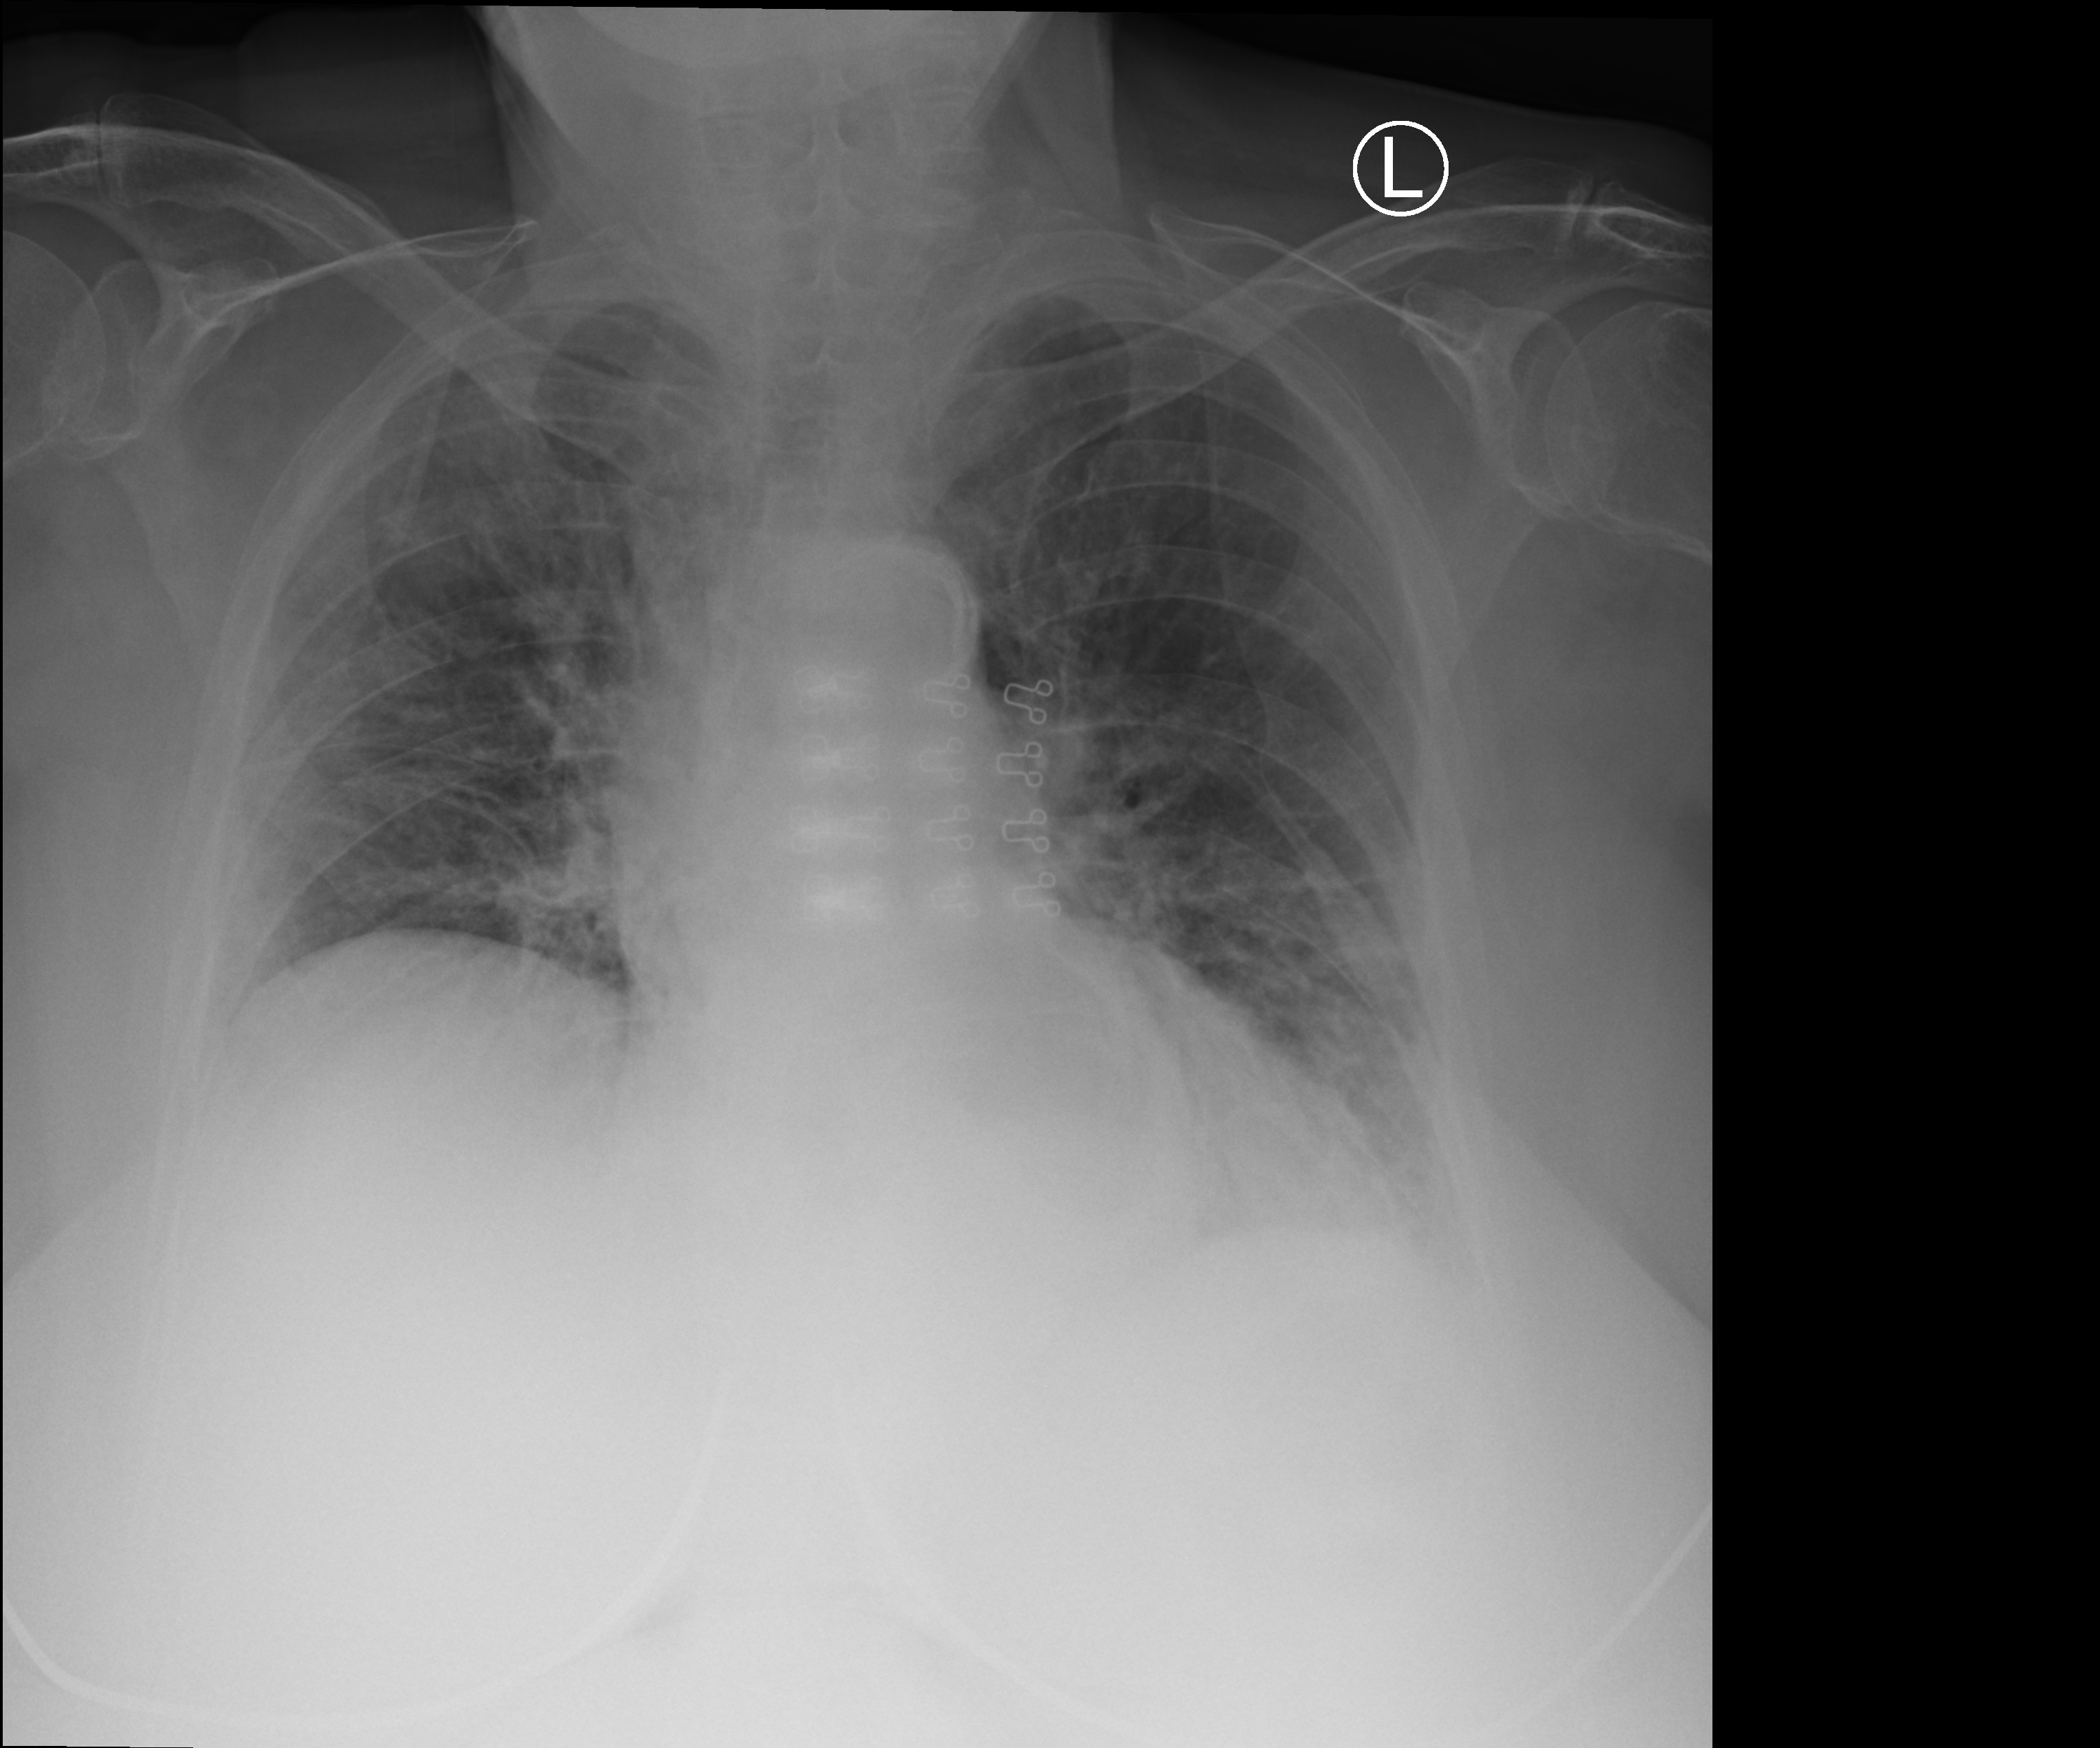
Portable chest radiograph; anteroposterior (AP) projection. Female patient hospitalised with COVID-19, age 75–90 years.
Hospital-stay facts (about this admission, not read from this image; timing relative to this image not recorded):
- admitted to intensive care during this hospital stay: no